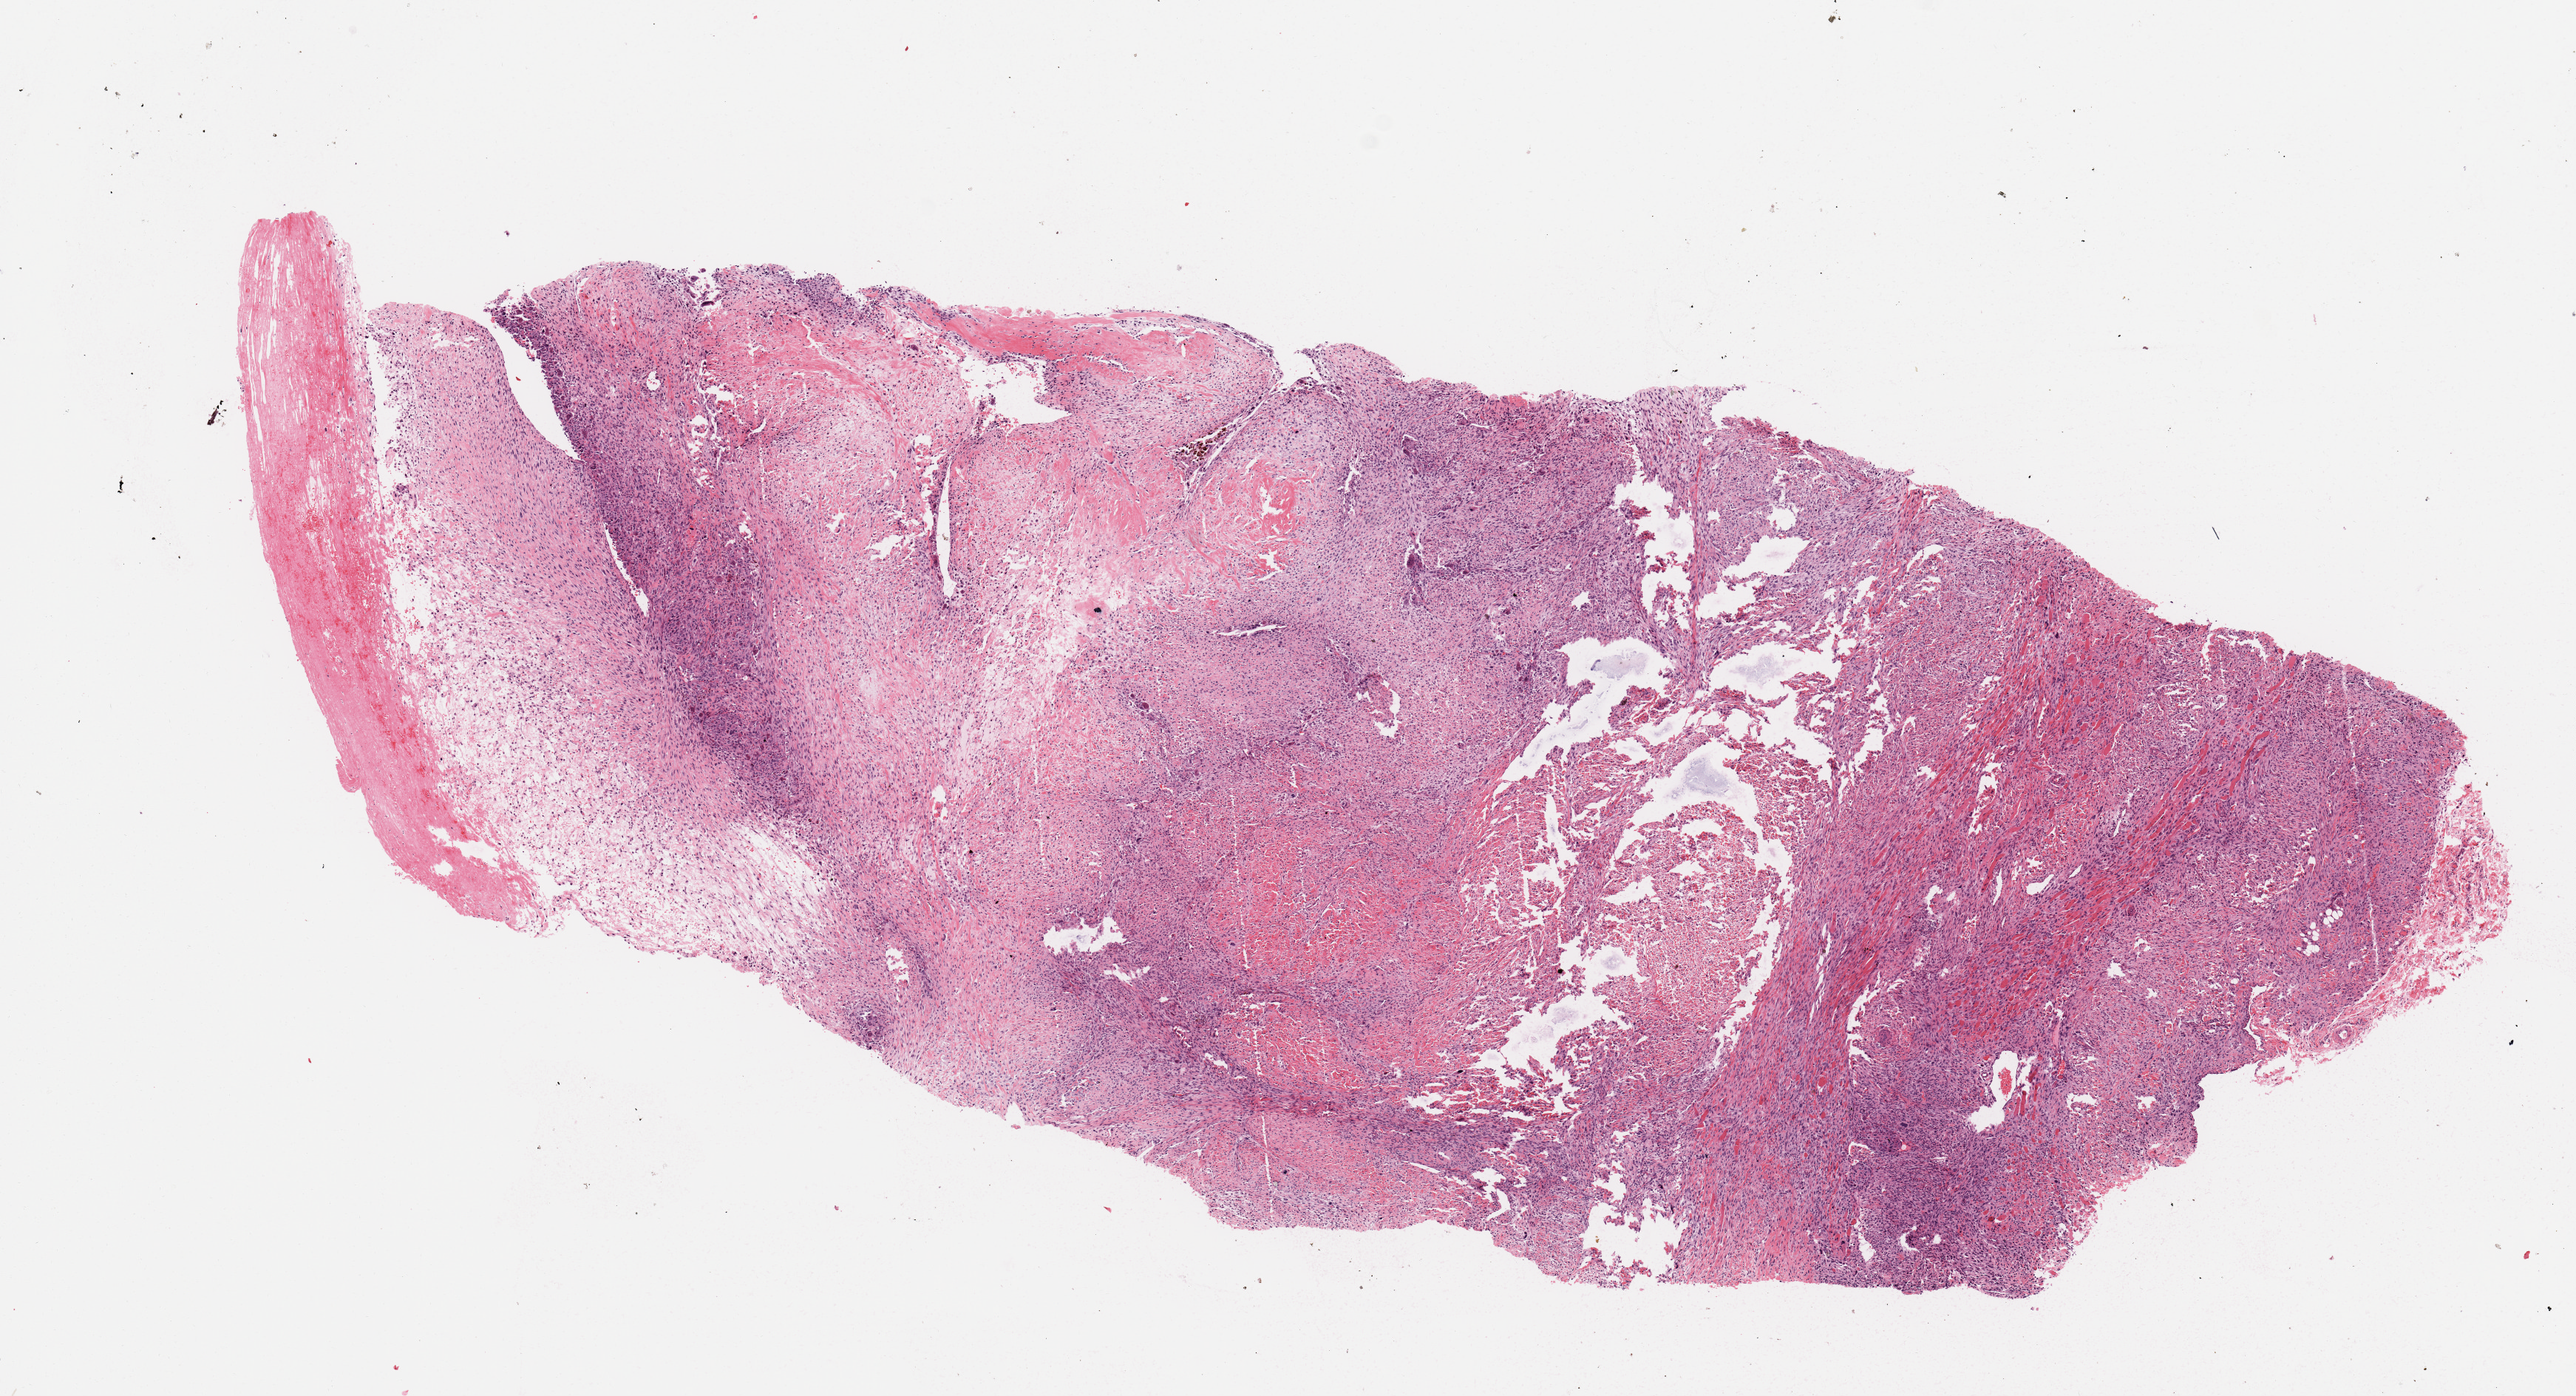
Digitized H&E-stained tissue section (whole slide), shown as a low-resolution overview of the whole scanned area (about 13.8 x 7.5 mm, from a 20x scan). Tumour tissue sample. Patient: male, age 54 years.
Patient diagnosis (cohort enrolment): sarcoma (site not recorded at cohort level). Primary tumour site (as recorded): upper extremity.